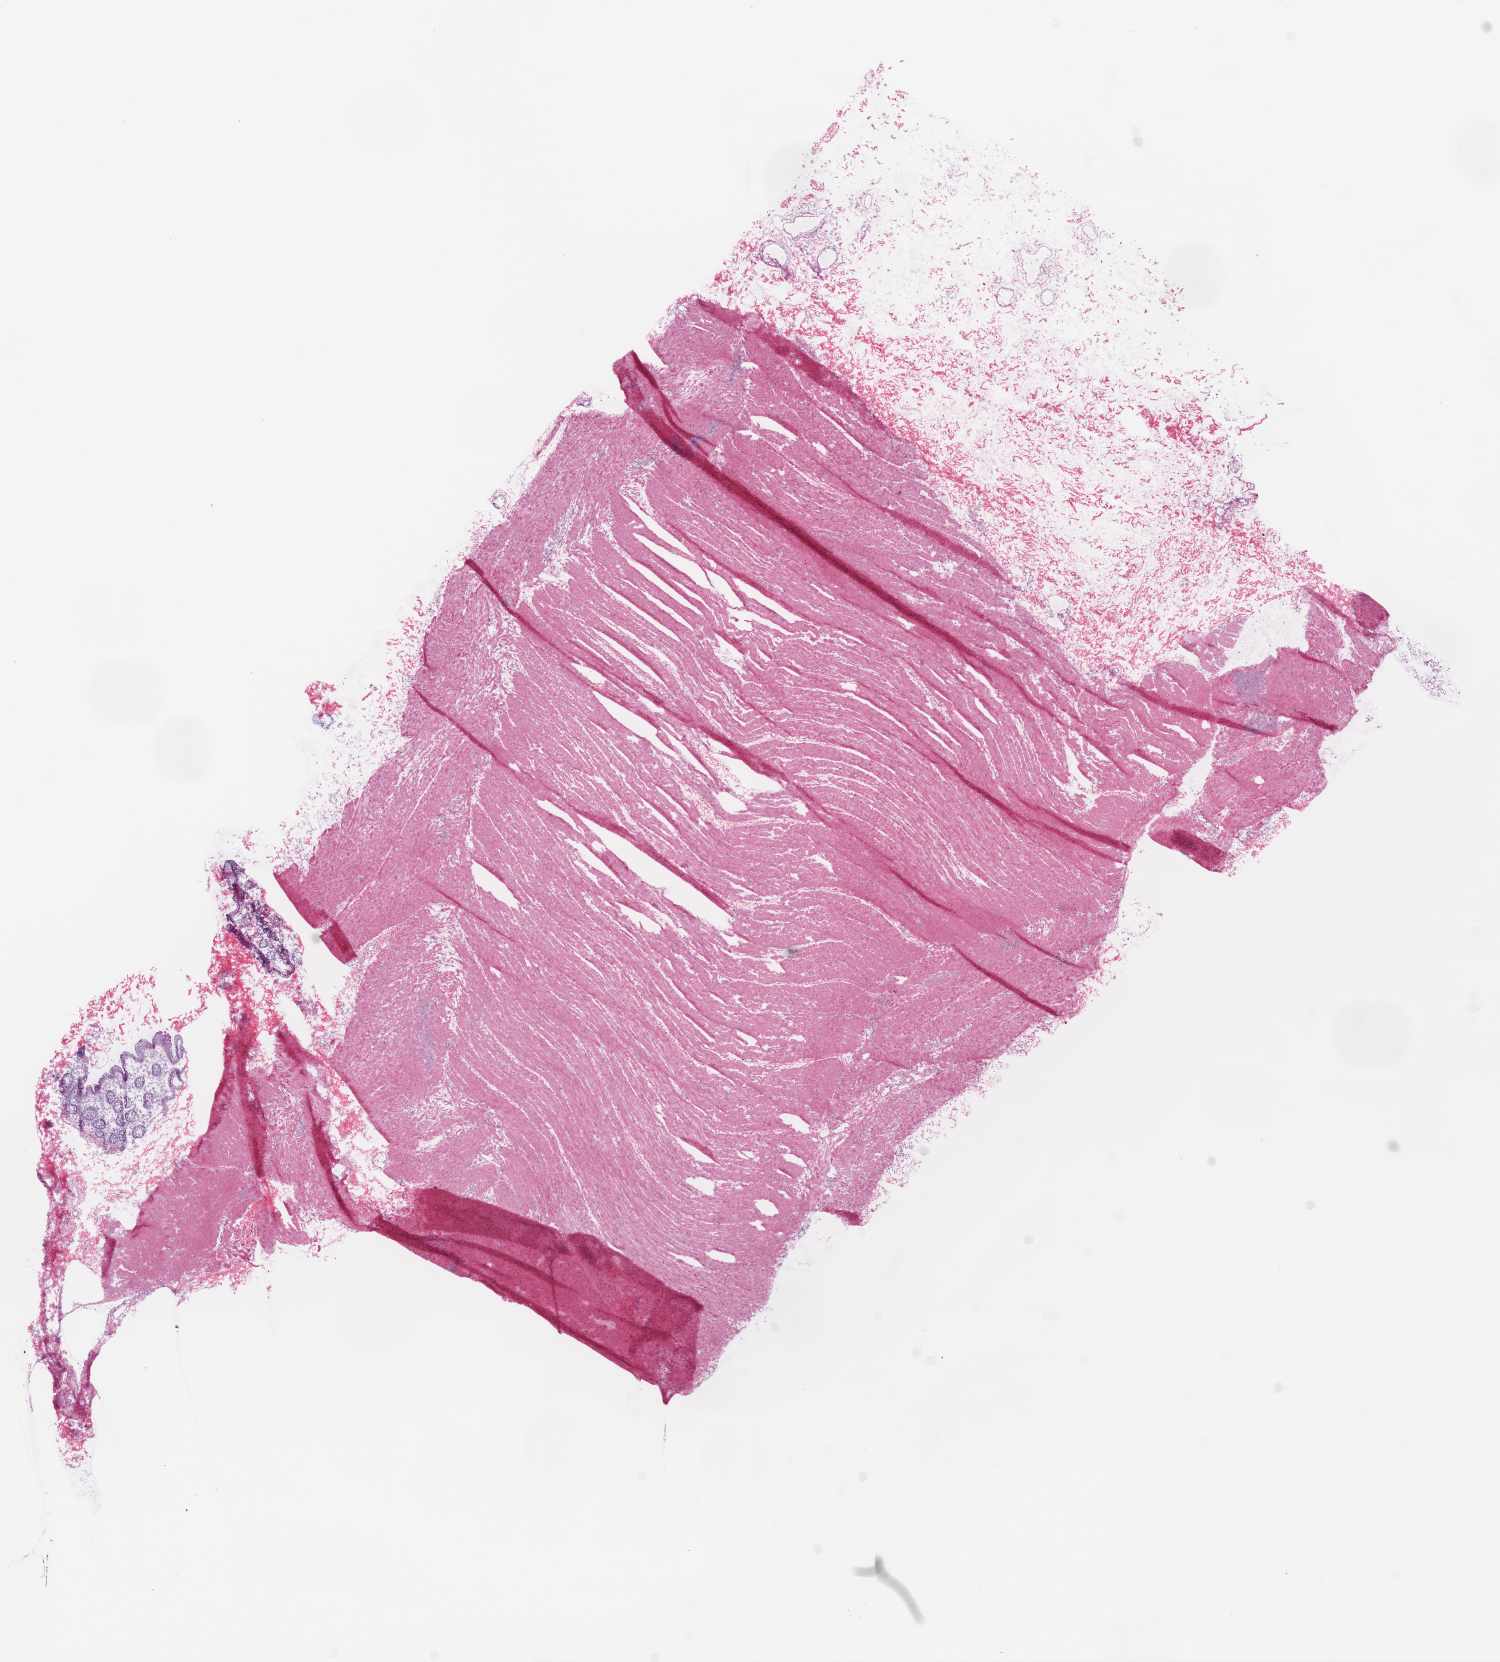
Whole-slide histology image, H&E, whole scanned area (about 12.0 x 13.3 mm, slide scanned at 20x) shown as a low-resolution overview, frozen section, sample: solid tissue normal (non-tumour tissue), colon. Patient: female, age at initial diagnosis 71 years.
• this section: solid tissue normal sample (biorepository sample class)
• patient diagnosis: Mucinous adenocarcinoma